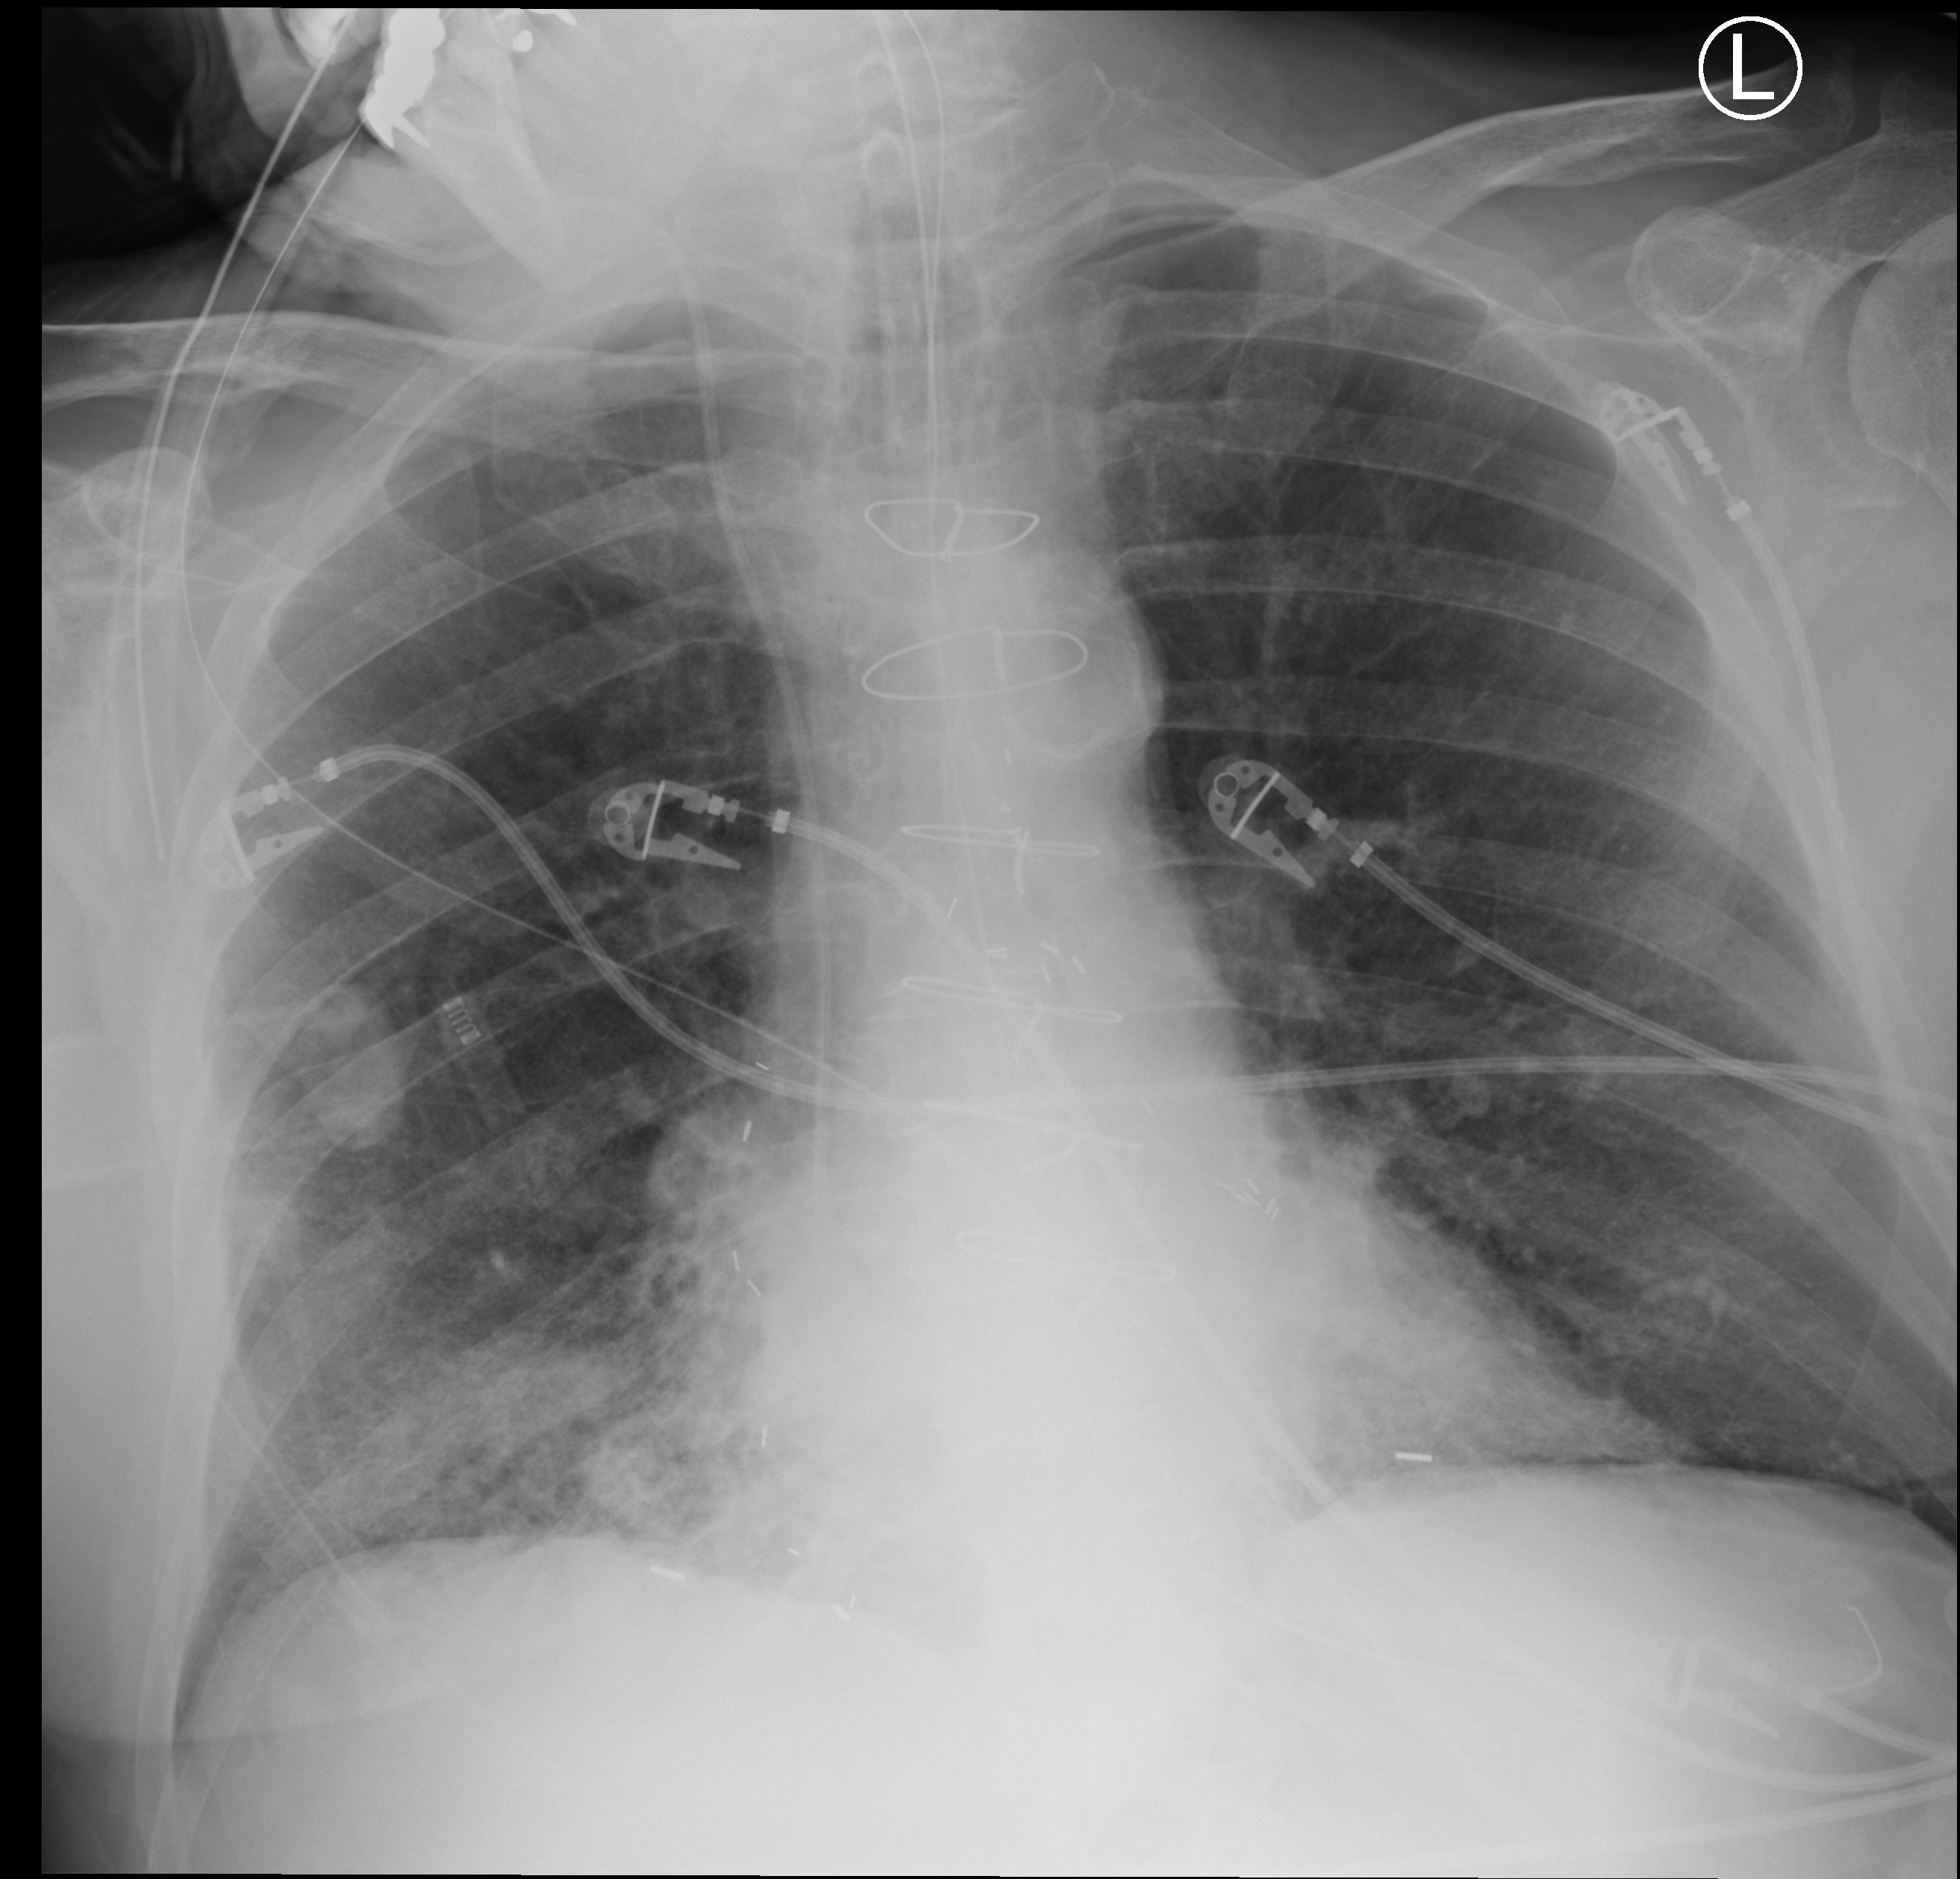
Chest X-ray (portable). Patient hospitalised with COVID-19; male, aged 75–90 years.
From the hospital-stay record, not from the radiograph (when in the stay this image was taken is not recorded):
- mechanically ventilated during this hospital stay: yes